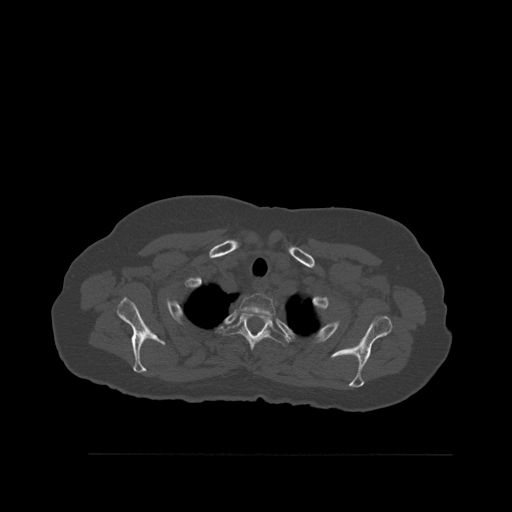
CT including the spine, one axial slice; slice 435 of 527 in the series (ordered by position); bone window (W 1800 / L 400 HU); 1.5 mm slice thickness; 512 × 512 image matrix, field of view 470 × 470 mm. Female patient, age 73 years. From the clinical record (not read from this slice): primary cancer: breast; vertebrae with lytic lesions (as recorded): L2.
Structures marked on this image (semi-automatically segmented with operator editing):
- T1 vertebra: bounding box (x1, y1, x2, y2) in pixels: (240, 294, 276, 318)
- T2 vertebra: (221, 311, 290, 352)